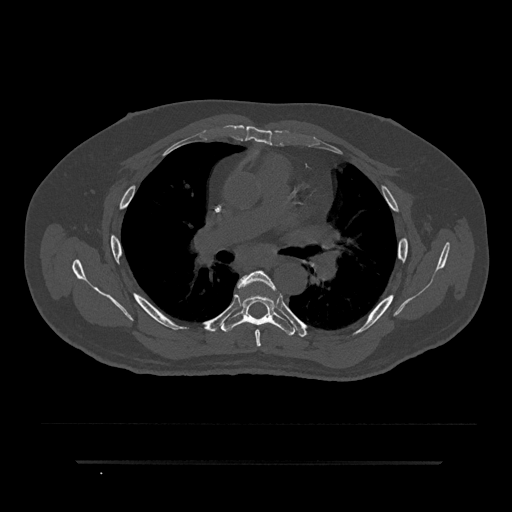
CT including the spine, one axial slice. Reconstruction kernel Br40s/3. 120 kVp. Bone window (W 1800 / L 400 HU). 512 × 512 image matrix, field of view 464 × 464 mm. Male patient, age 59 years. From the clinical record (not read from this slice): primary cancer: bile ducts; vertebrae with lytic lesions (as recorded): T10.
Outlined on this slice (semi-automatically segmented with operator editing):
- T5 vertebra: bounding box [x1, y1, x2, y2] px = [238, 271, 276, 347]
- T6 vertebra: [221, 295, 294, 336]